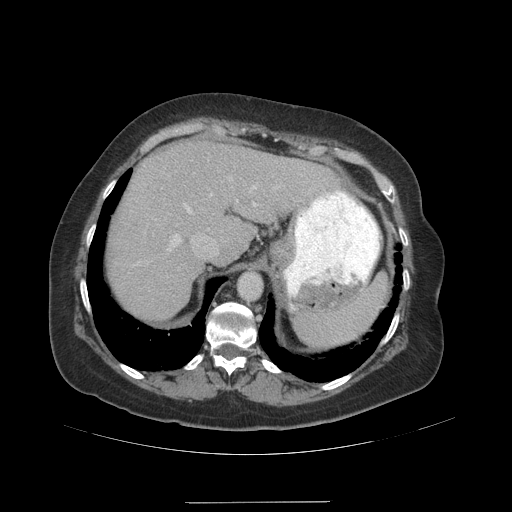
Contrast-enhanced abdominal CT (liver protocol), one axial slice; position 76 of 99 along the scan axis; reconstruction kernel STANDARD; soft-tissue window (W 400 / L 40 HU); 512 × 512 image matrix, field of view 440 × 440 mm. Case-level facts recorded for this patient, not image findings: diagnosis: hepatocellular carcinoma (patient treated with transarterial chemoembolisation; whether this scan precedes or follows treatment is not stated here); TNM stage (as recorded): Stage-IVA; Child-Pugh class: A; tumour nodularity: multinodular.
Structures marked on this image (semi-automatically segmented with operator editing):
- abdominal aorta: bounding box (x1, y1, x2, y2) in pixels: (238, 272, 261, 301)
- liver parenchyma outside the tumour (the mass and vessels are separate outlines, so this box may not span the whole liver): (108, 140, 336, 320)
- liver vessels: (167, 186, 257, 251)